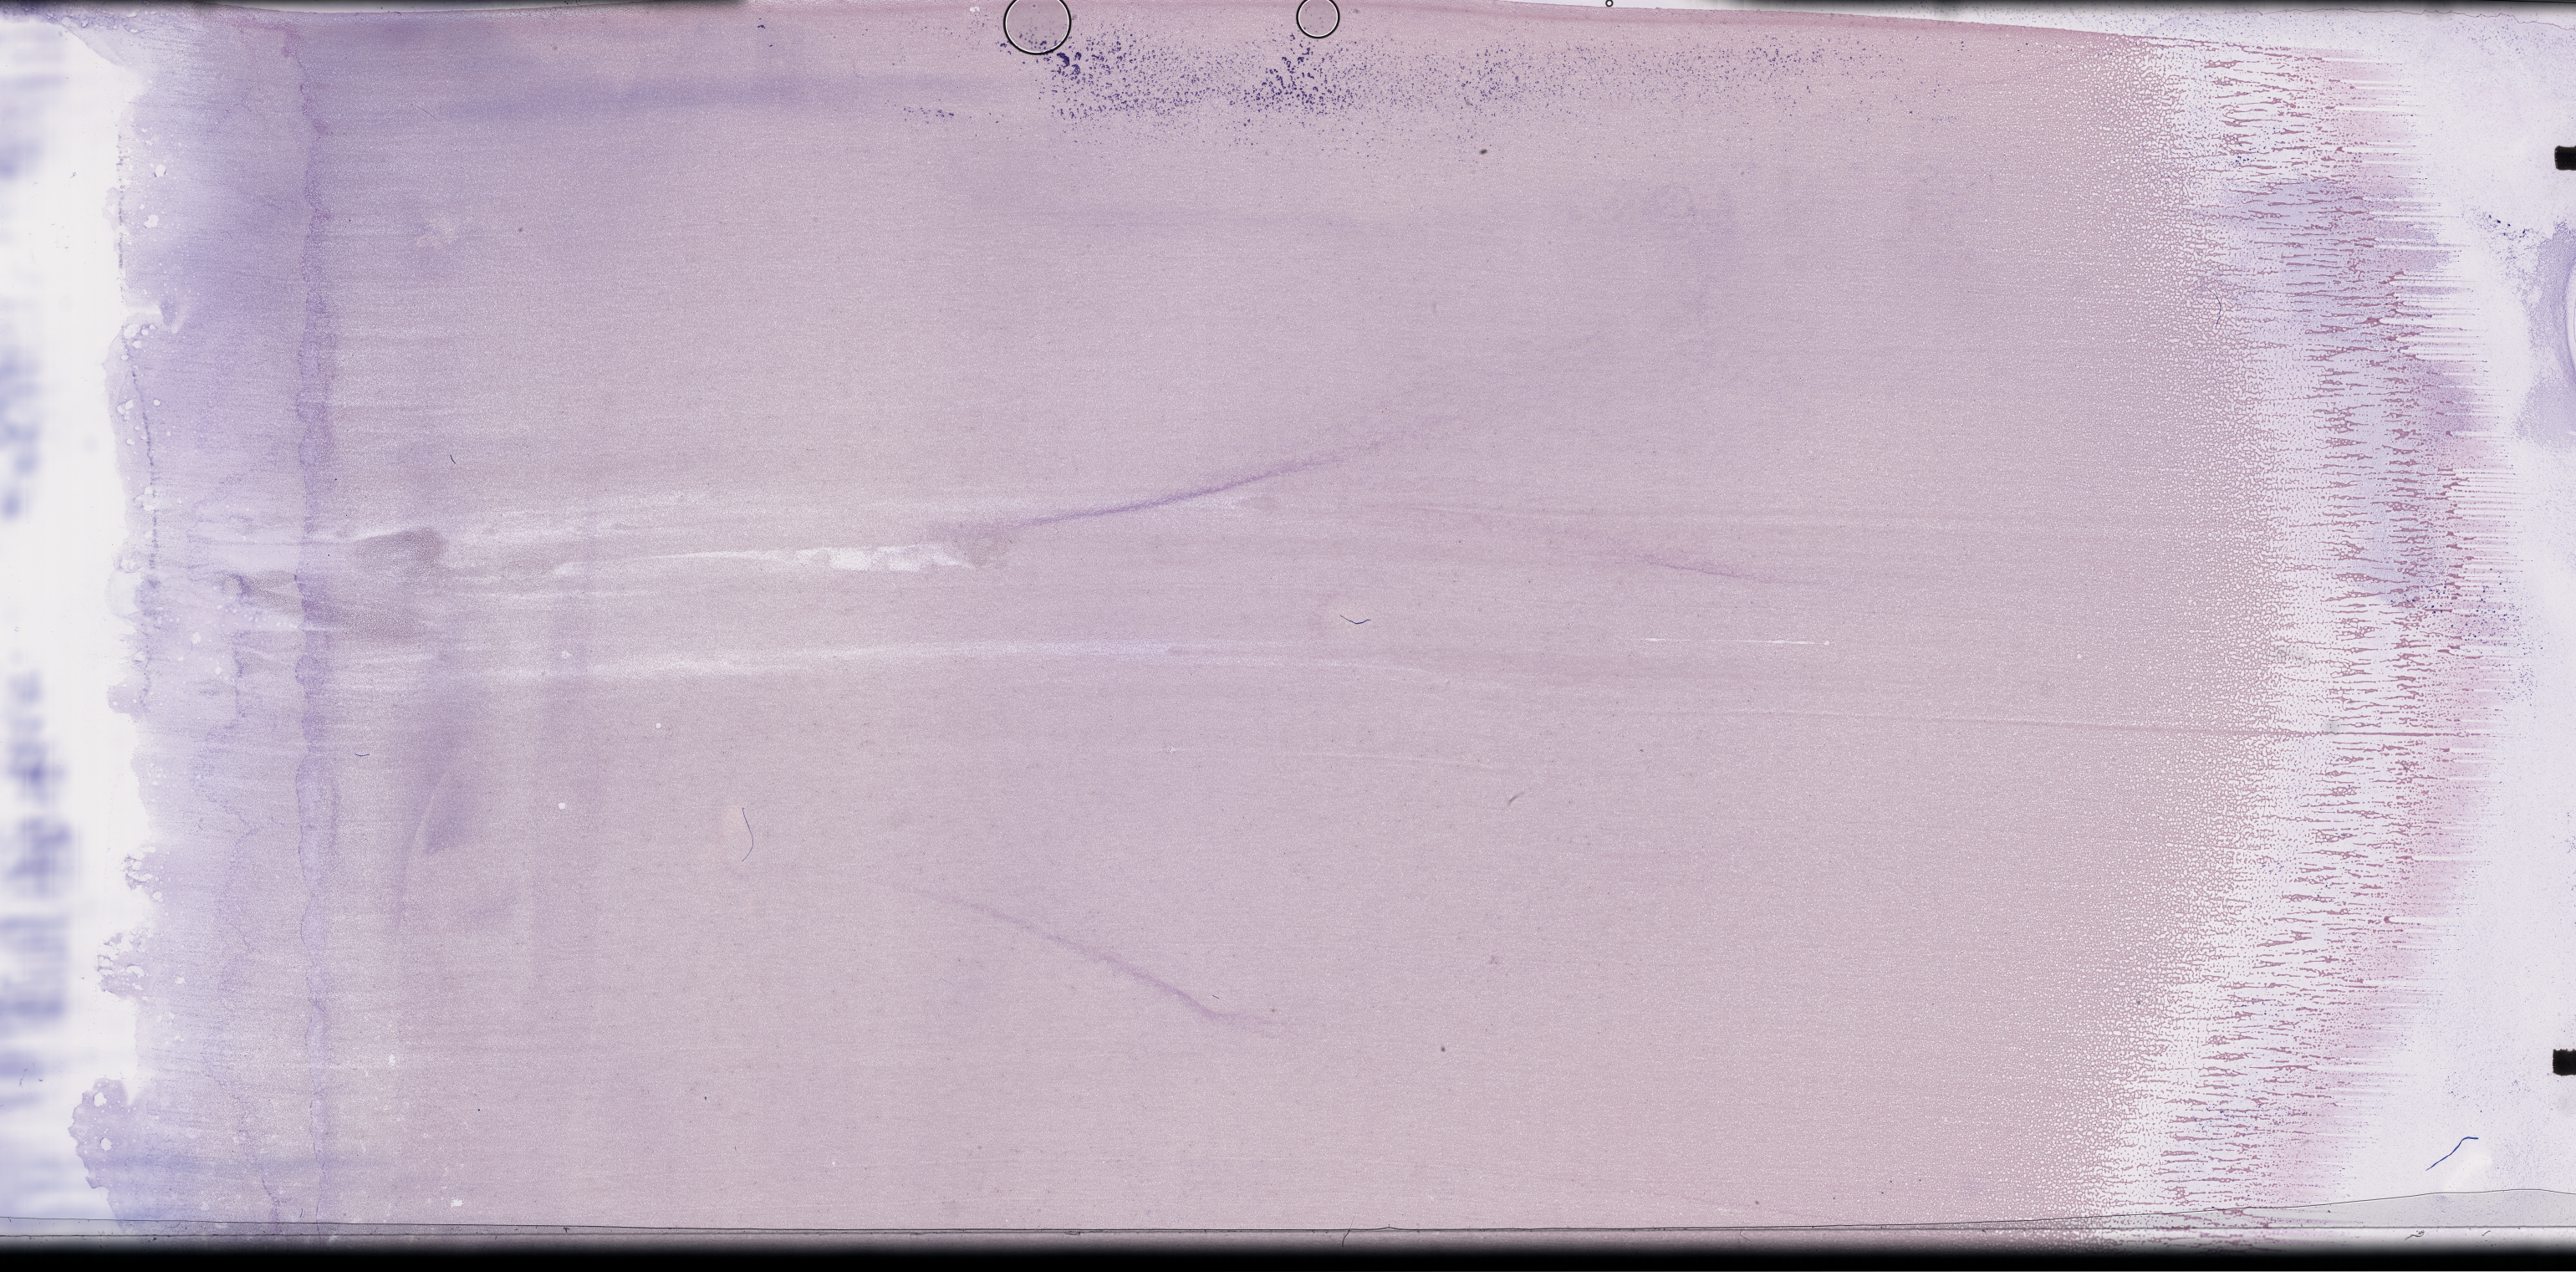
Whole-slide image of a whole blood smear, Wright-Giemsa stain — shown as a low-resolution overview of the whole scanned area (about 49.8 x 24.6 mm); EDTA-anticoagulated smear. Patient sex: female.
Patient diagnosis: Plasma Cell Myeloma.